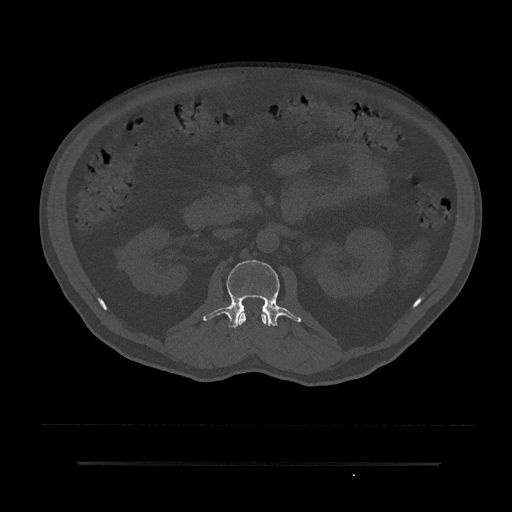
CT including the spine, one axial slice; slice 91 of 797 in the series (ordered by position); bone window (W 1800 / L 400 HU); 0.5 mm slice thickness; 512 × 512 image matrix. Patient: male, 59 years. From the clinical record (not read from this slice): primary cancer: bile ducts; vertebrae with lytic lesions (as recorded): T10.
Outlined on this slice (semi-automatic segmentation, software-assisted and operator-edited):
- L1 vertebra: bounding box [x1, y1, x2, y2] px = [238, 311, 267, 326]
- L2 vertebra: [203, 260, 301, 328]